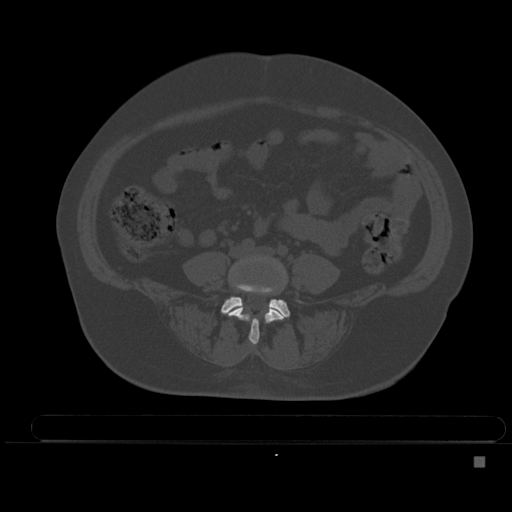
CT including the spine, one axial slice. Slice 119 of 495 in the series (ordered by position). Bone window (W 1800 / L 400 HU). 1.5 mm slice thickness. 512 × 512 image matrix. Female patient, age 33 years. From the clinical record (not read from this slice): primary cancer: breast.
Outlined on this slice (semi-automatic segmentation, software-assisted and operator-edited):
- L4 vertebra: box from (x=228, y=256) to (x=287, y=345) px
- L5 vertebra: (x=221, y=285)–(x=290, y=318)